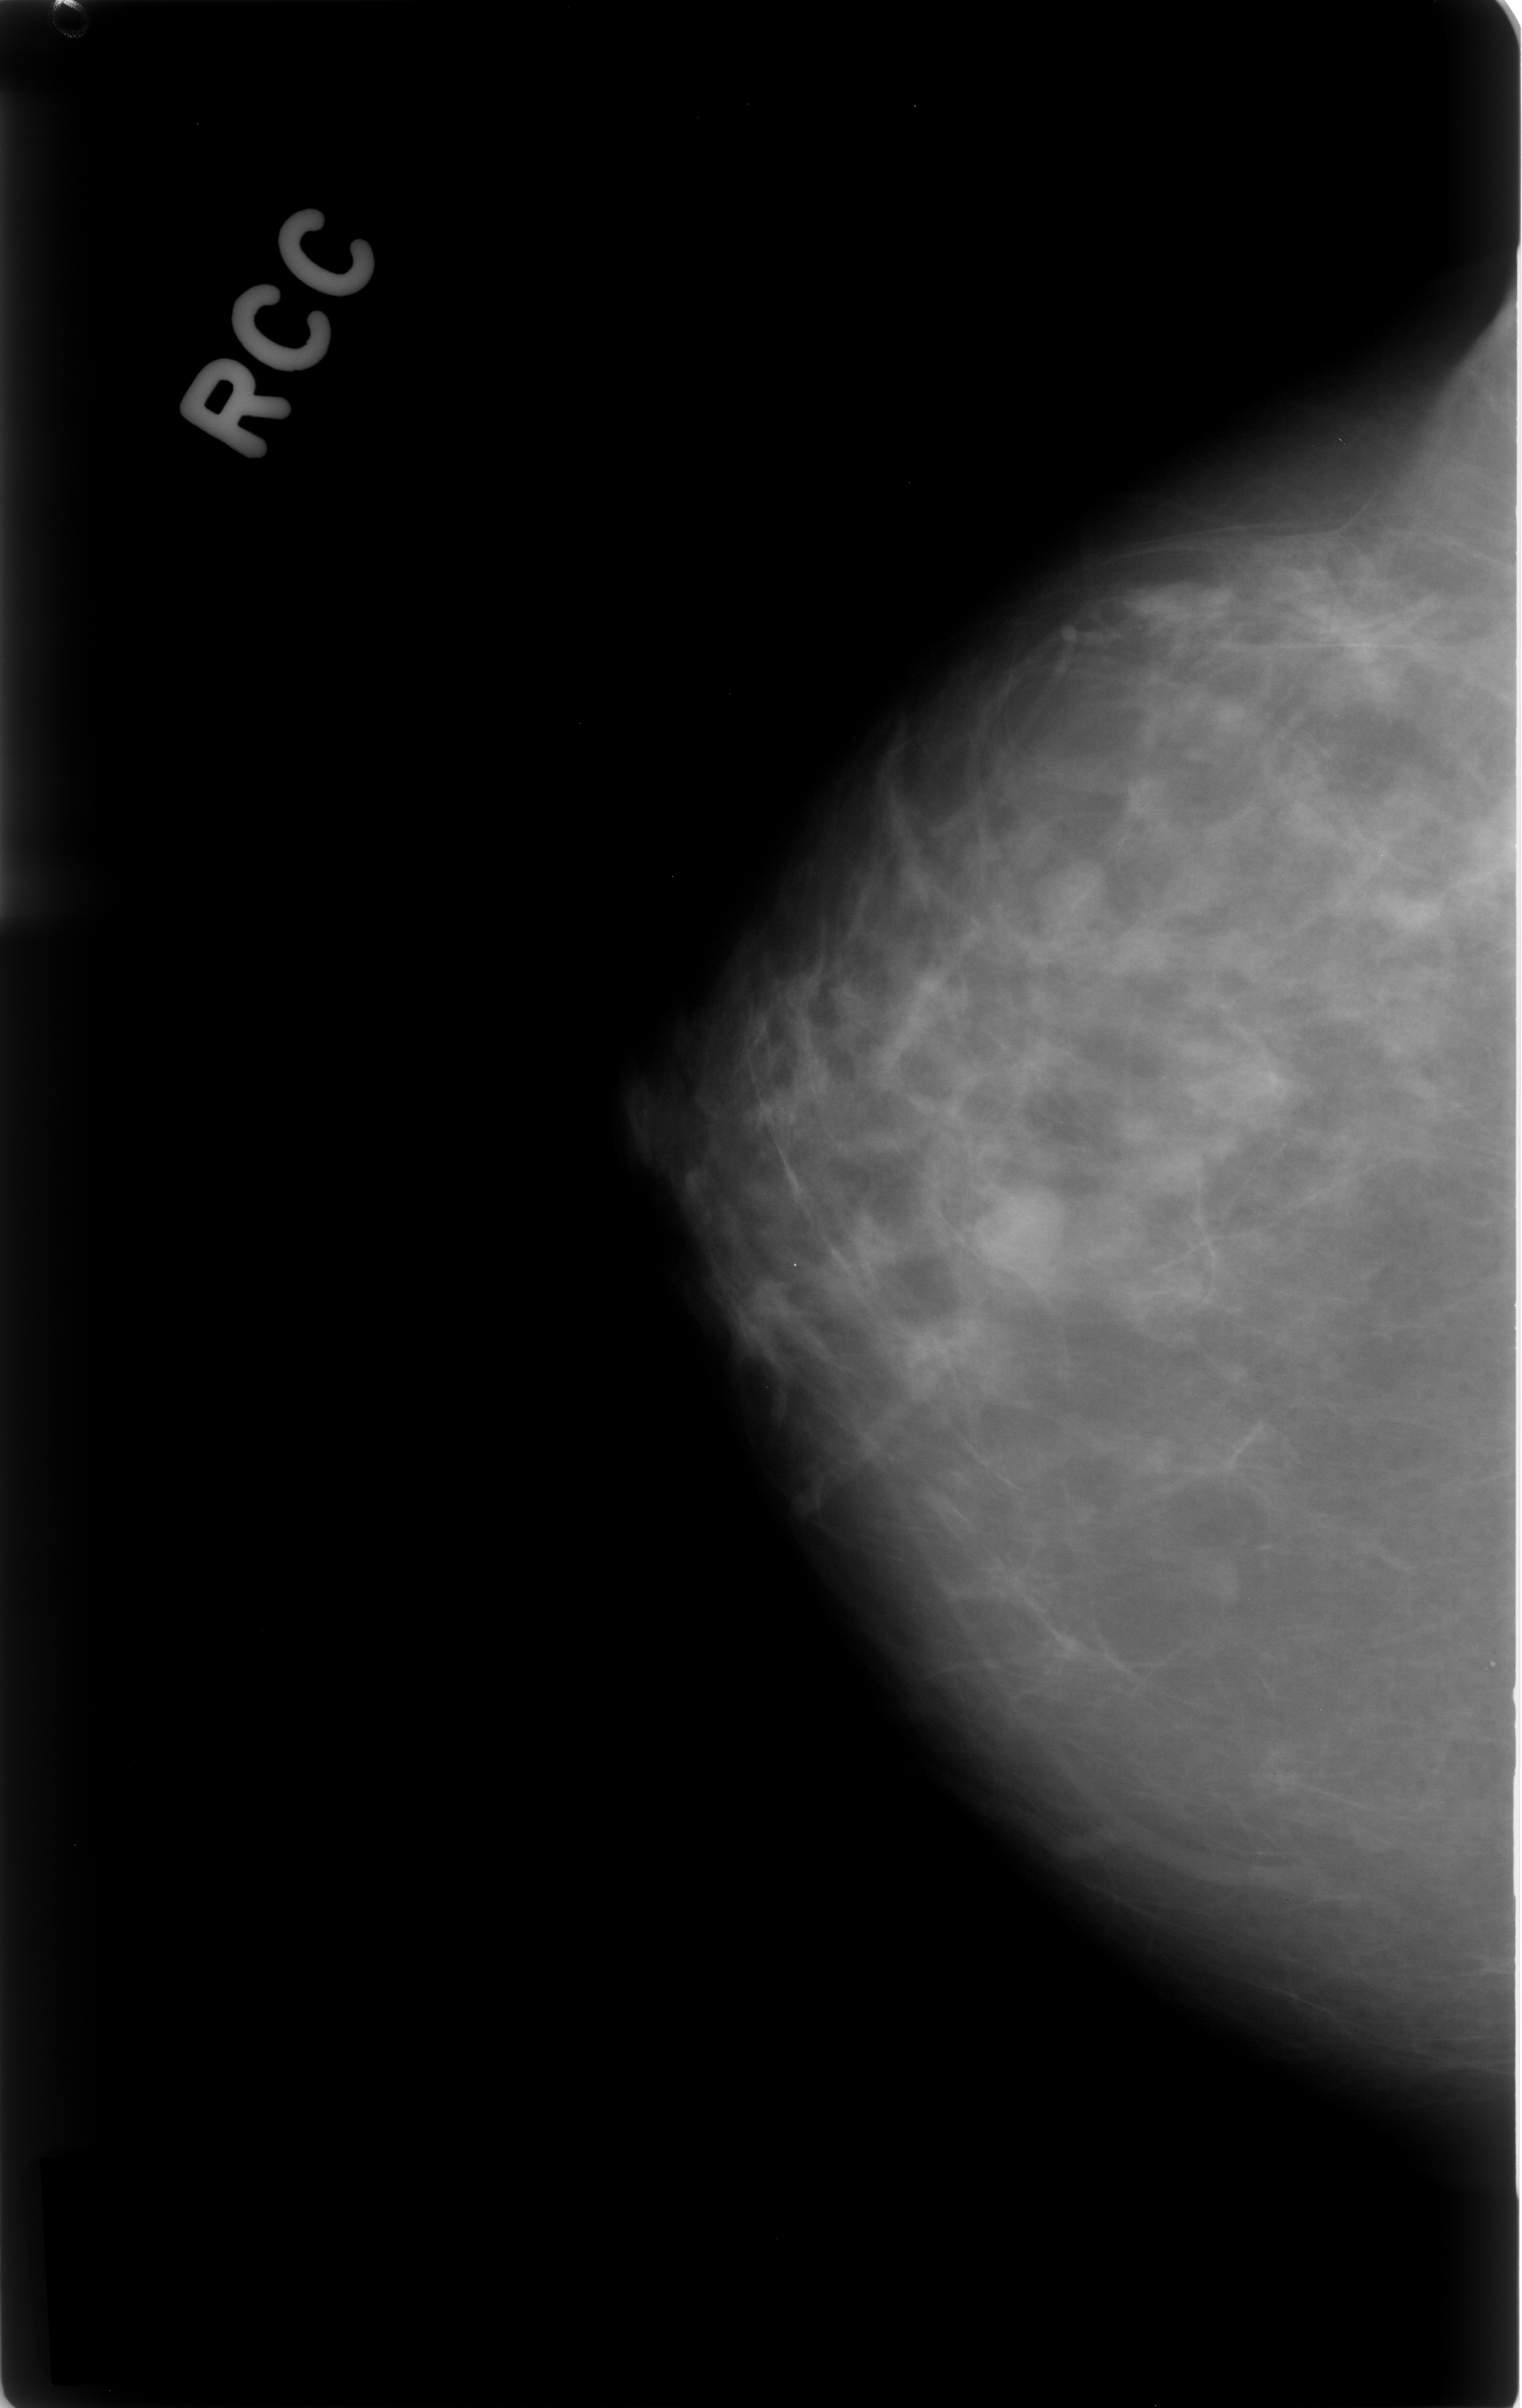
Digitized screen-film mammogram; right breast; CC view.
- Abnormality record for this image: mass, shape oval, margins circumscribed; BI-RADS assessment category 3; pathology (as recorded): benign.